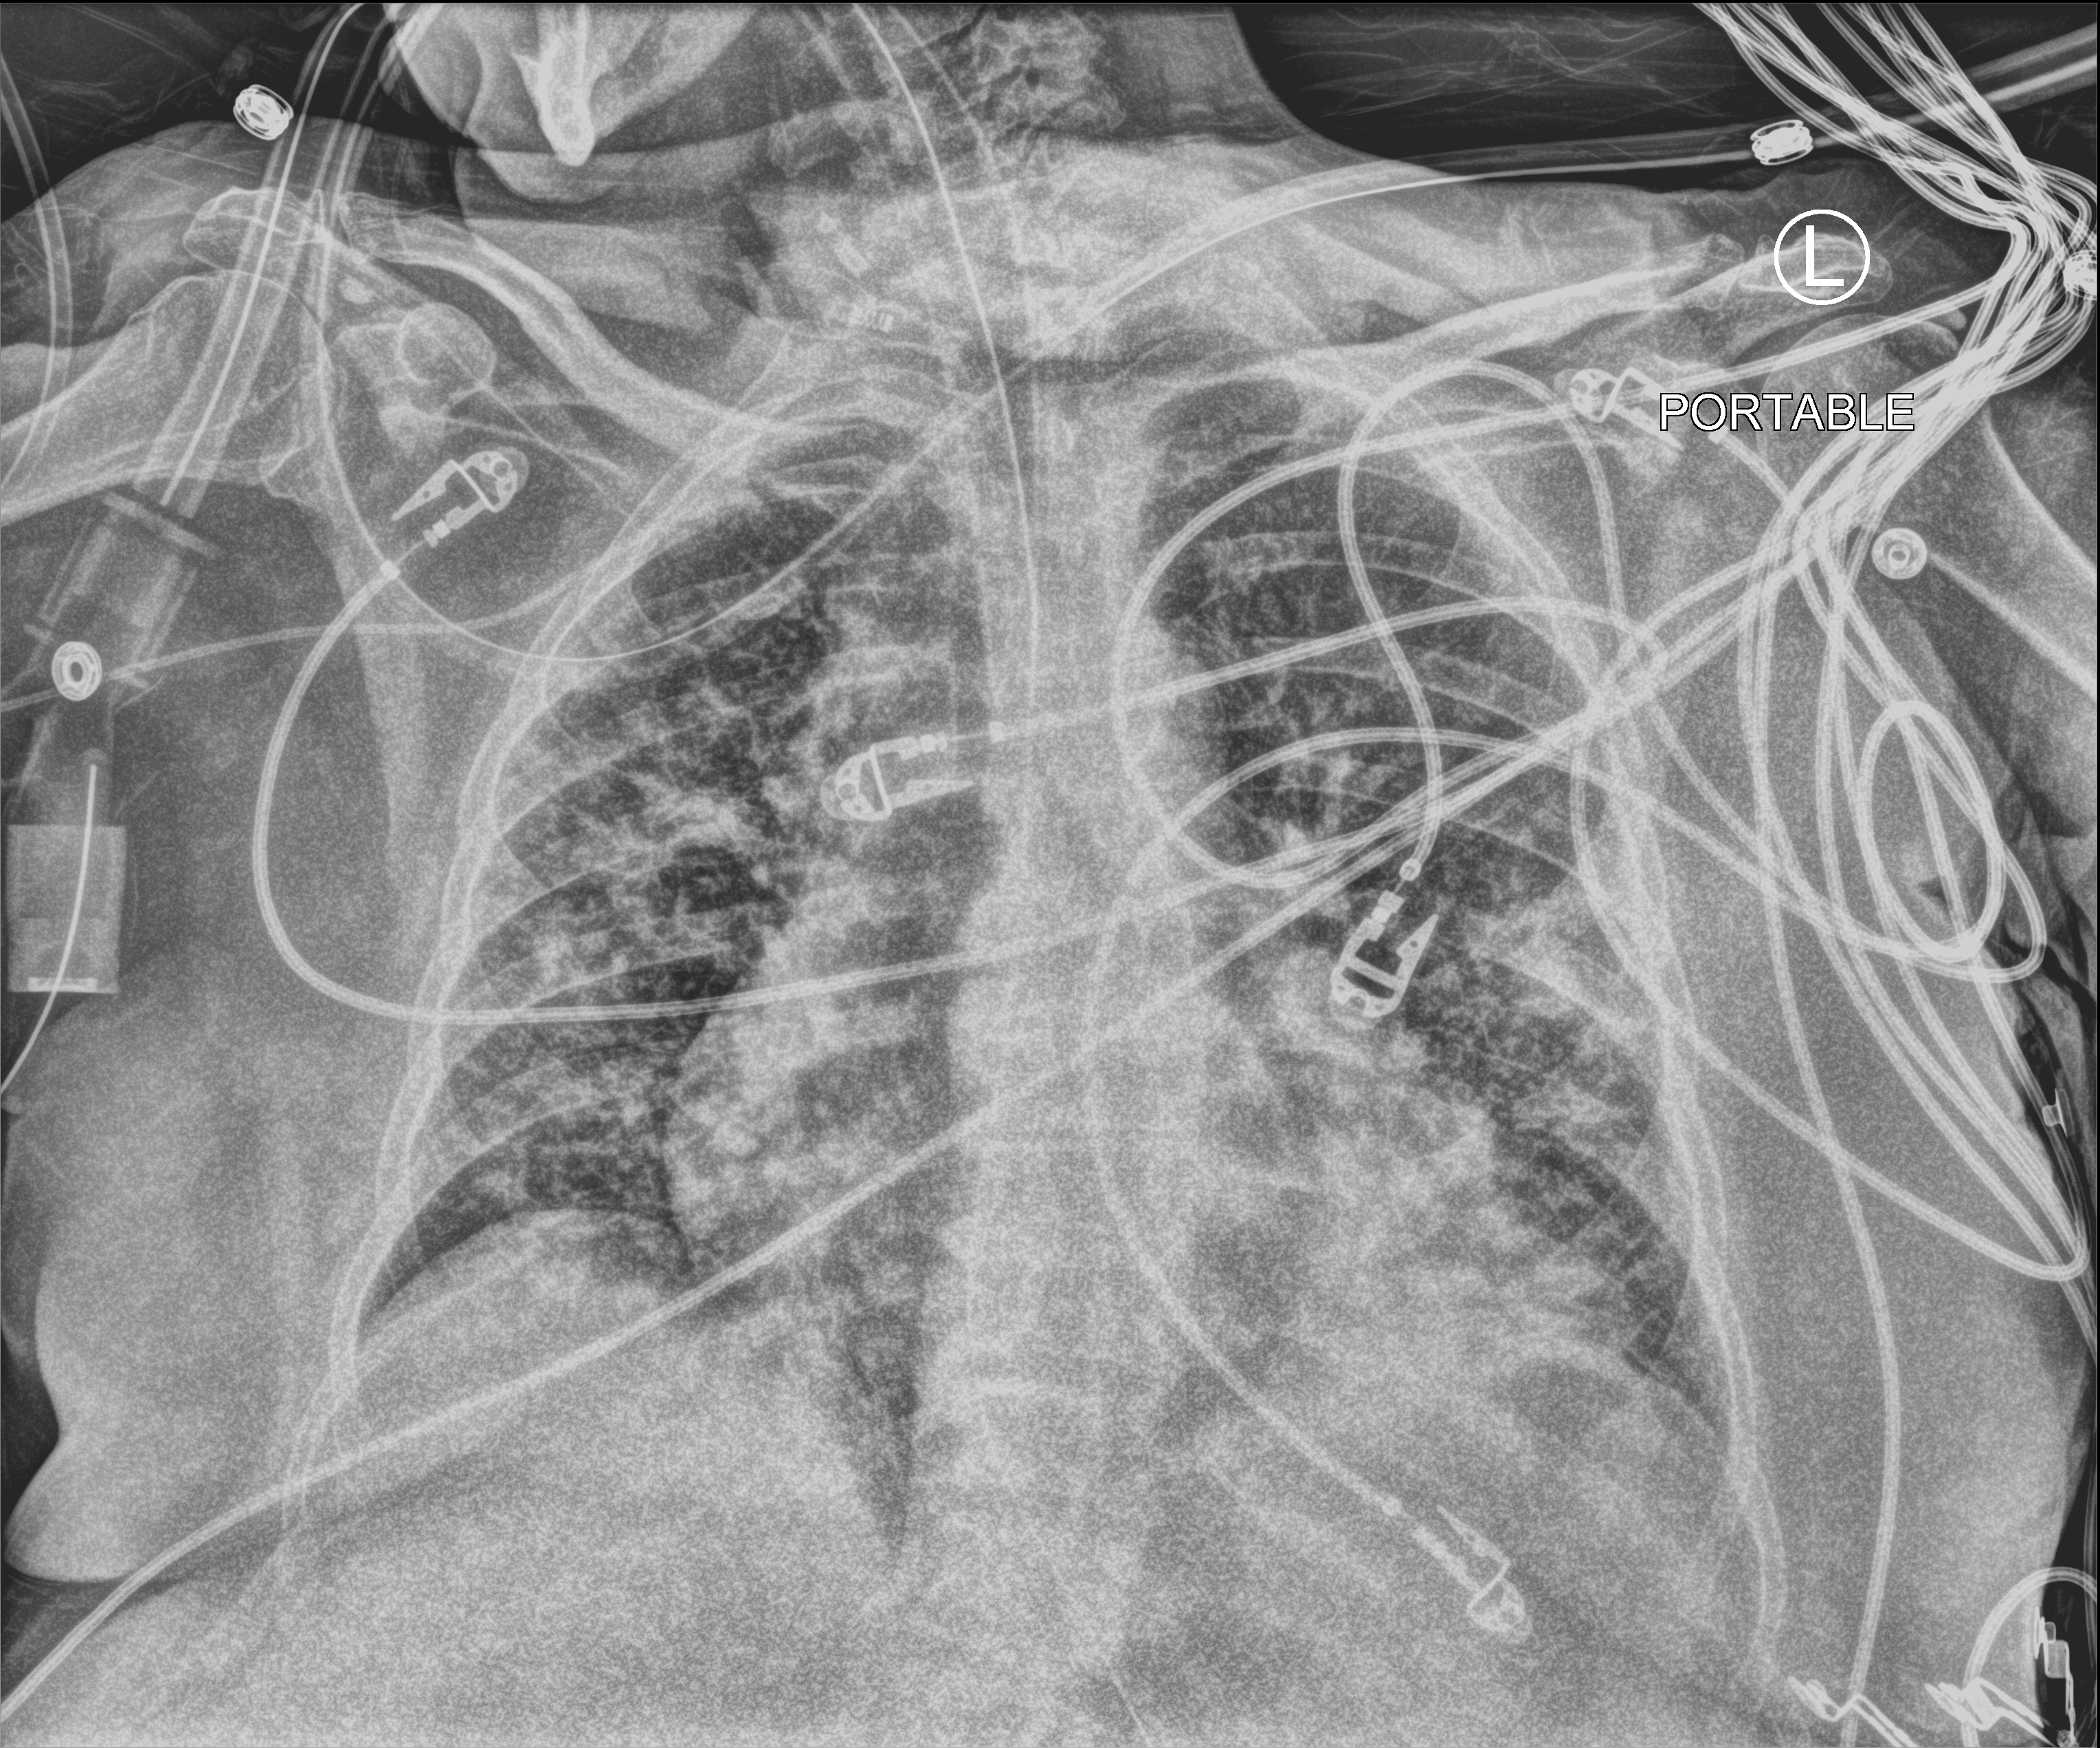
Bedside chest radiograph (computed radiography); anteroposterior (AP) projection. Female patient hospitalised with COVID-19, age 75–90 years.
From the hospital-stay record, not from the radiograph (when in the stay this image was taken is not recorded):
- mechanically ventilated during this hospital stay: yes